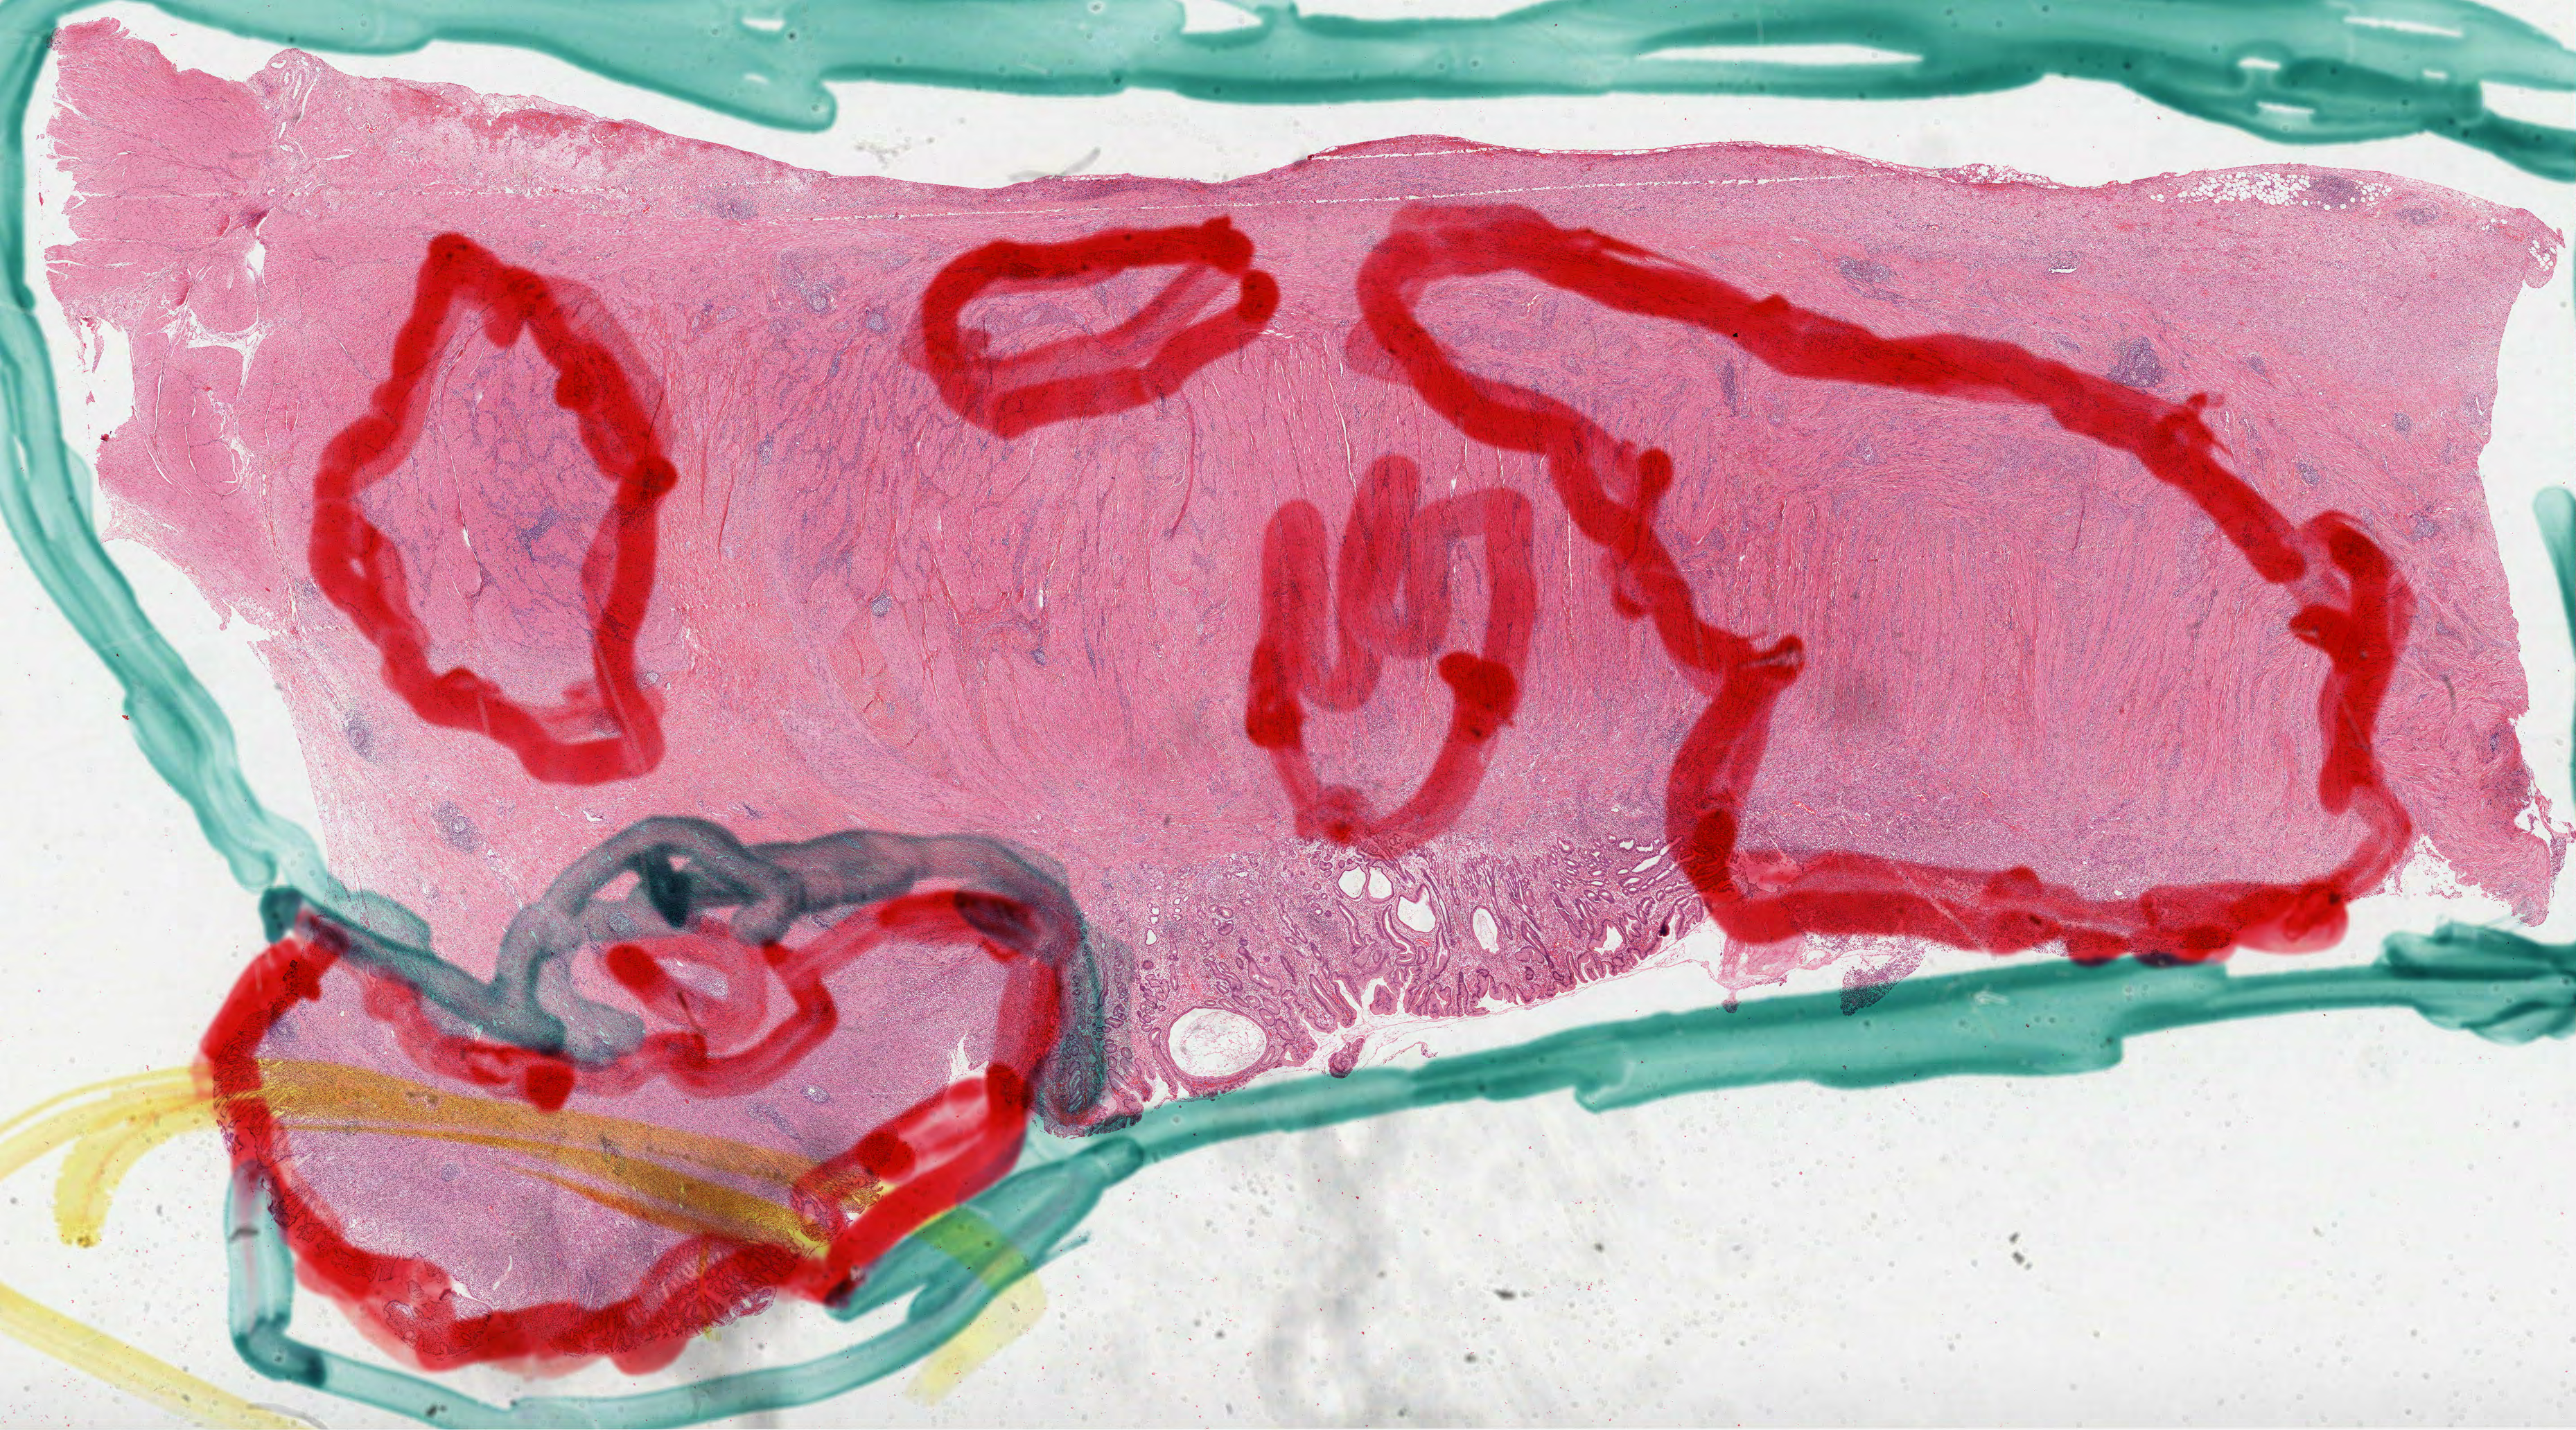
Digitized H&E-stained tissue section (whole slide), whole scanned area (about 30.0 x 16.6 mm) shown as a low-resolution overview. Formalin-fixed paraffin-embedded (FFPE) diagnostic section. Sample: primary tumour, stomach. Female patient; age at initial diagnosis 53 years. Histologic grade: G3 (poorly differentiated).
AJCC pathologic stage: IIIB (7th edition). TNM: T4a N2 M0. Lymph nodes positive (case pathology): 3 of 8 examined. Pathologic diagnosis: Adenocarcinoma, NOS.